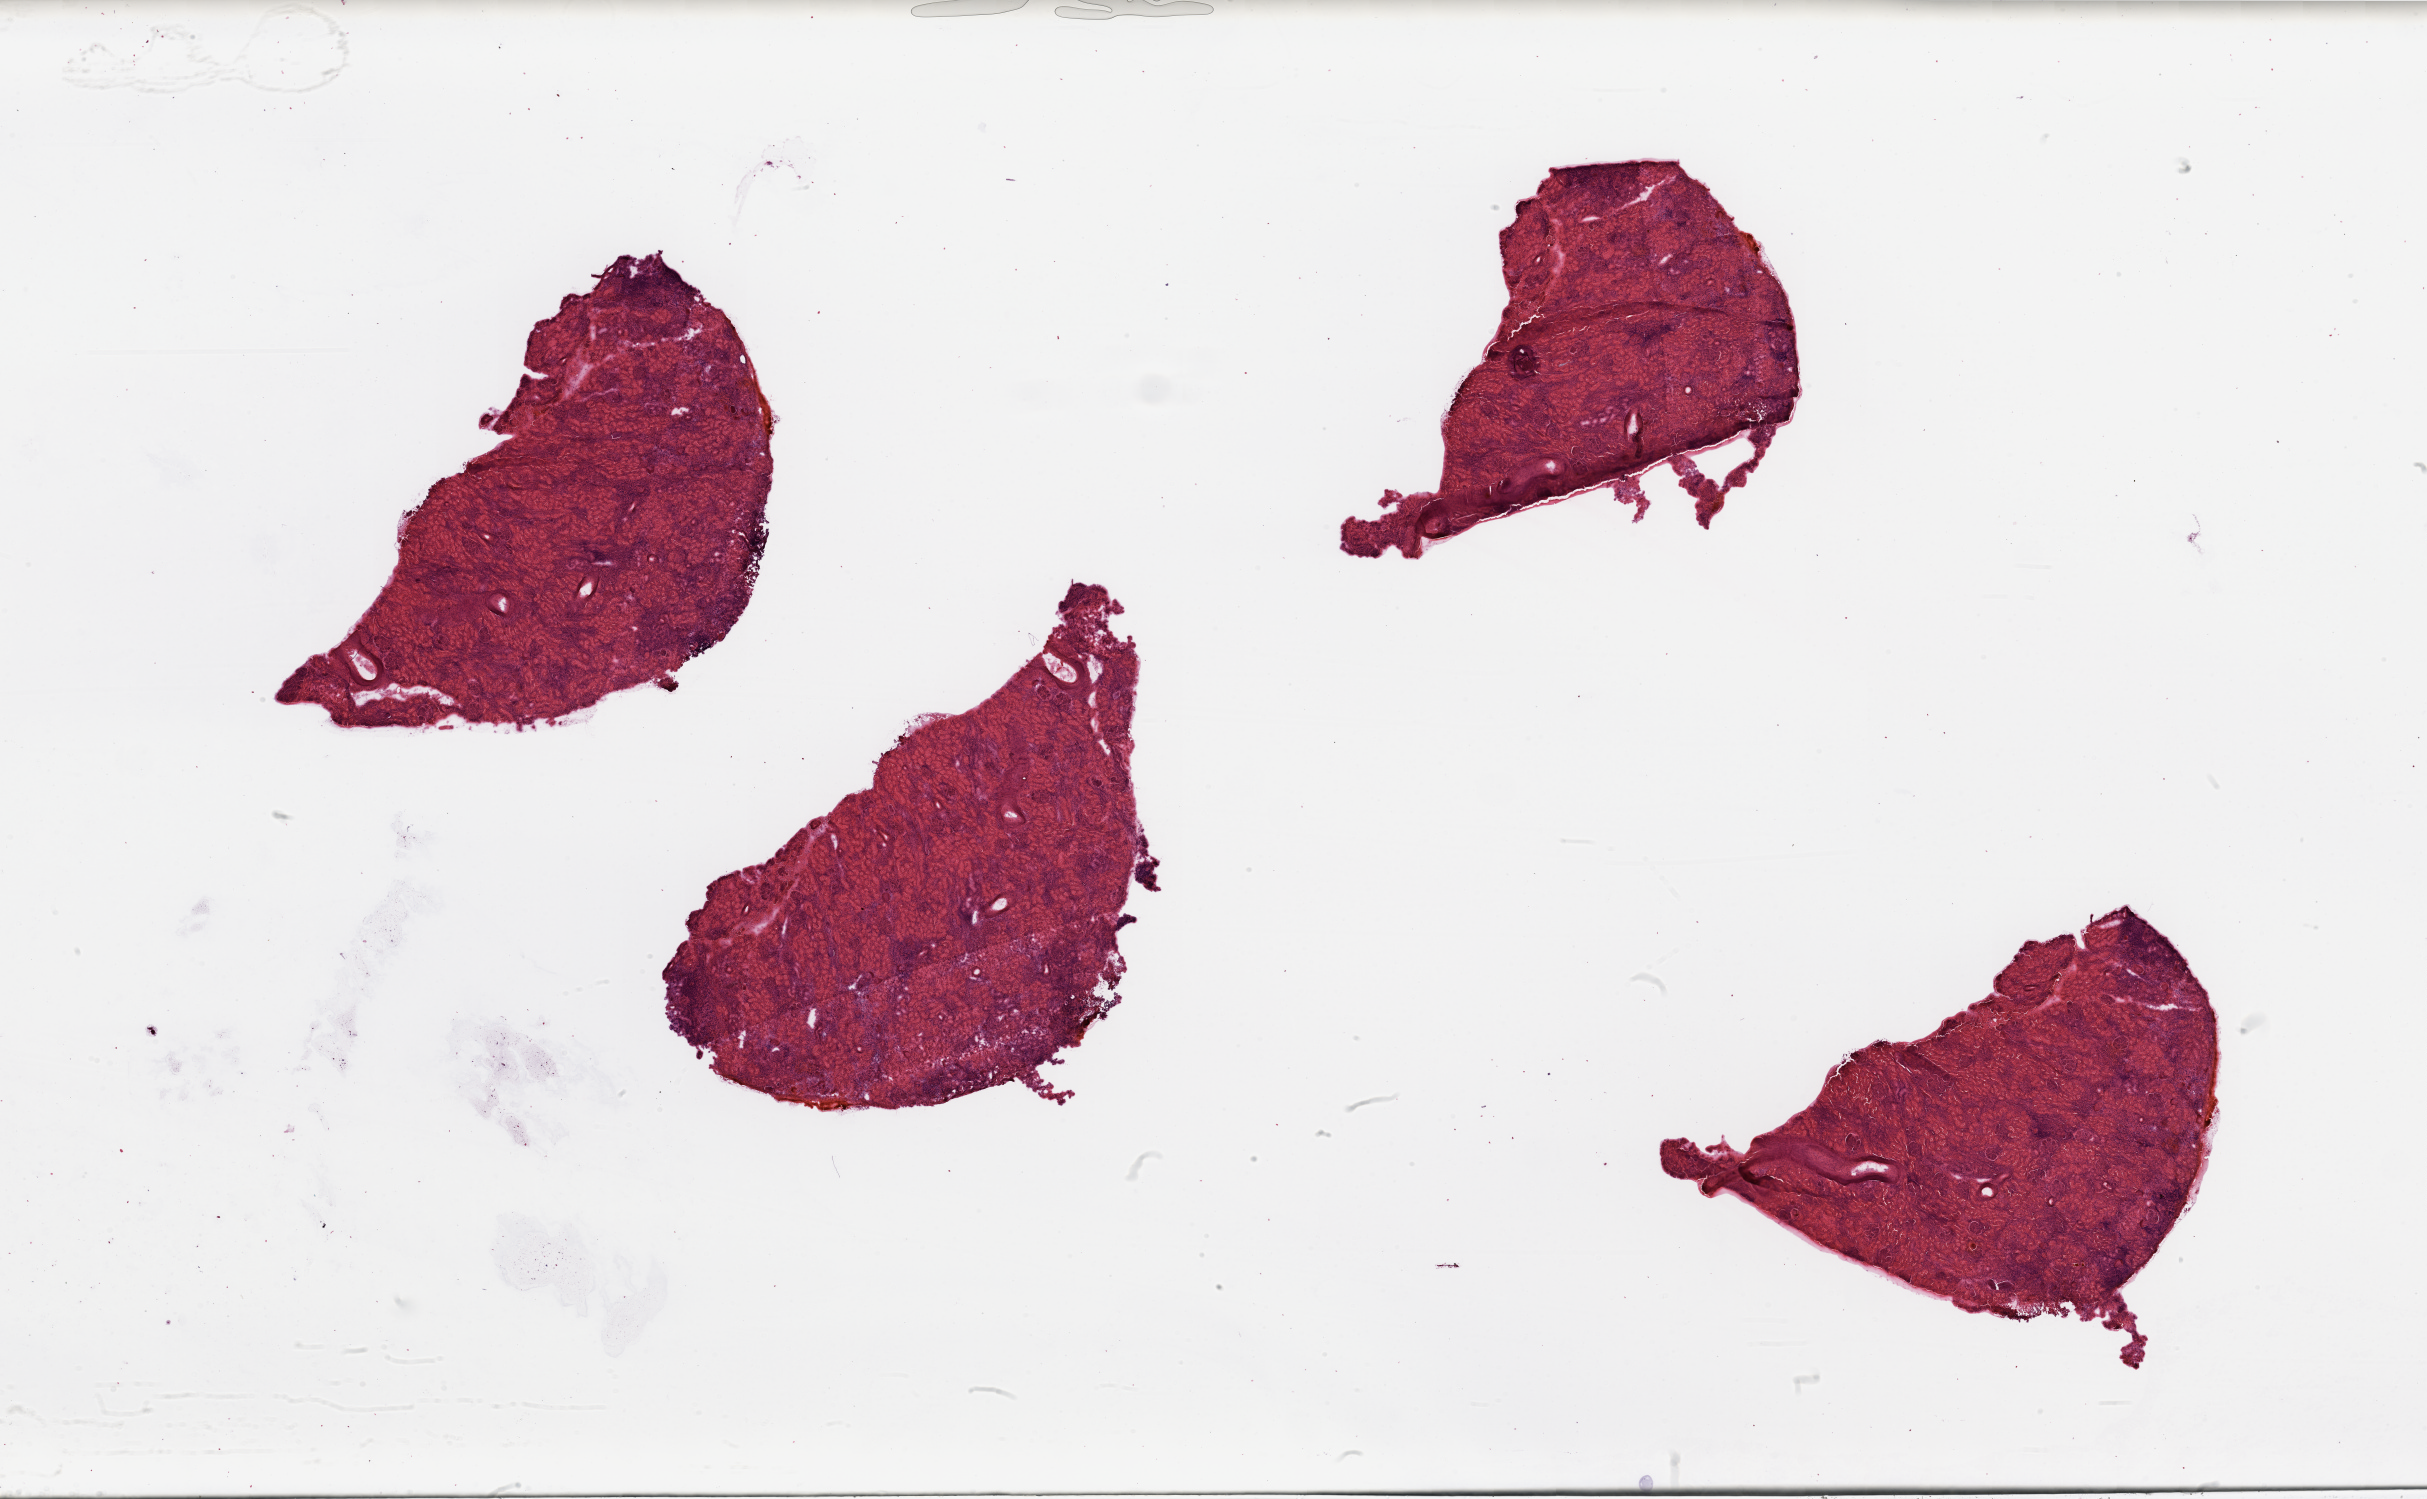
H&E whole-slide image, low-resolution overview of the scanned area, about 38.4 x 23.7 mm (from a 20x scan), normal (non-tumour) tissue sample, sampled site: kidney. Patient: female, age 74 years.
This section: normal (non-tumour) tissue from the same patient. Patient diagnosis: Renal cell carcinoma, NOS.